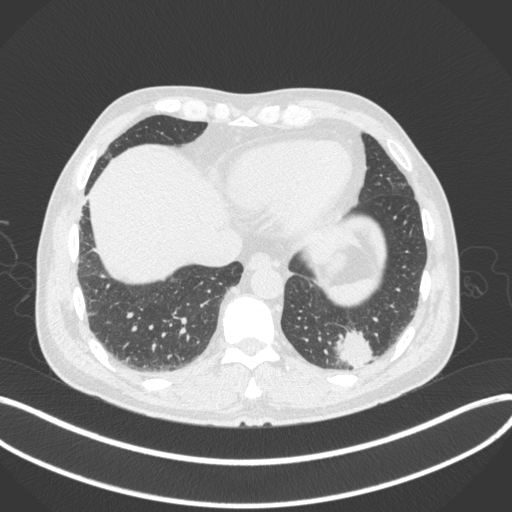
Chest CT, one axial slice. Slice 64 of 313 in the series (ordered by position). Lung window (W 1500 / L -600 HU). 1 mm slice thickness. 512 × 512 image matrix. Male patient, age 54 years. From the clinical record (not read from this slice): clinical TNM (as recorded): T1c N0 M1; histopathological grade: G3.
Outlined on this slice (bounding box drawn by a radiologist):
- lung tumour (recorded histology: adenocarcinoma): bounding box [x1, y1, x2, y2] px = [332, 326, 380, 373]